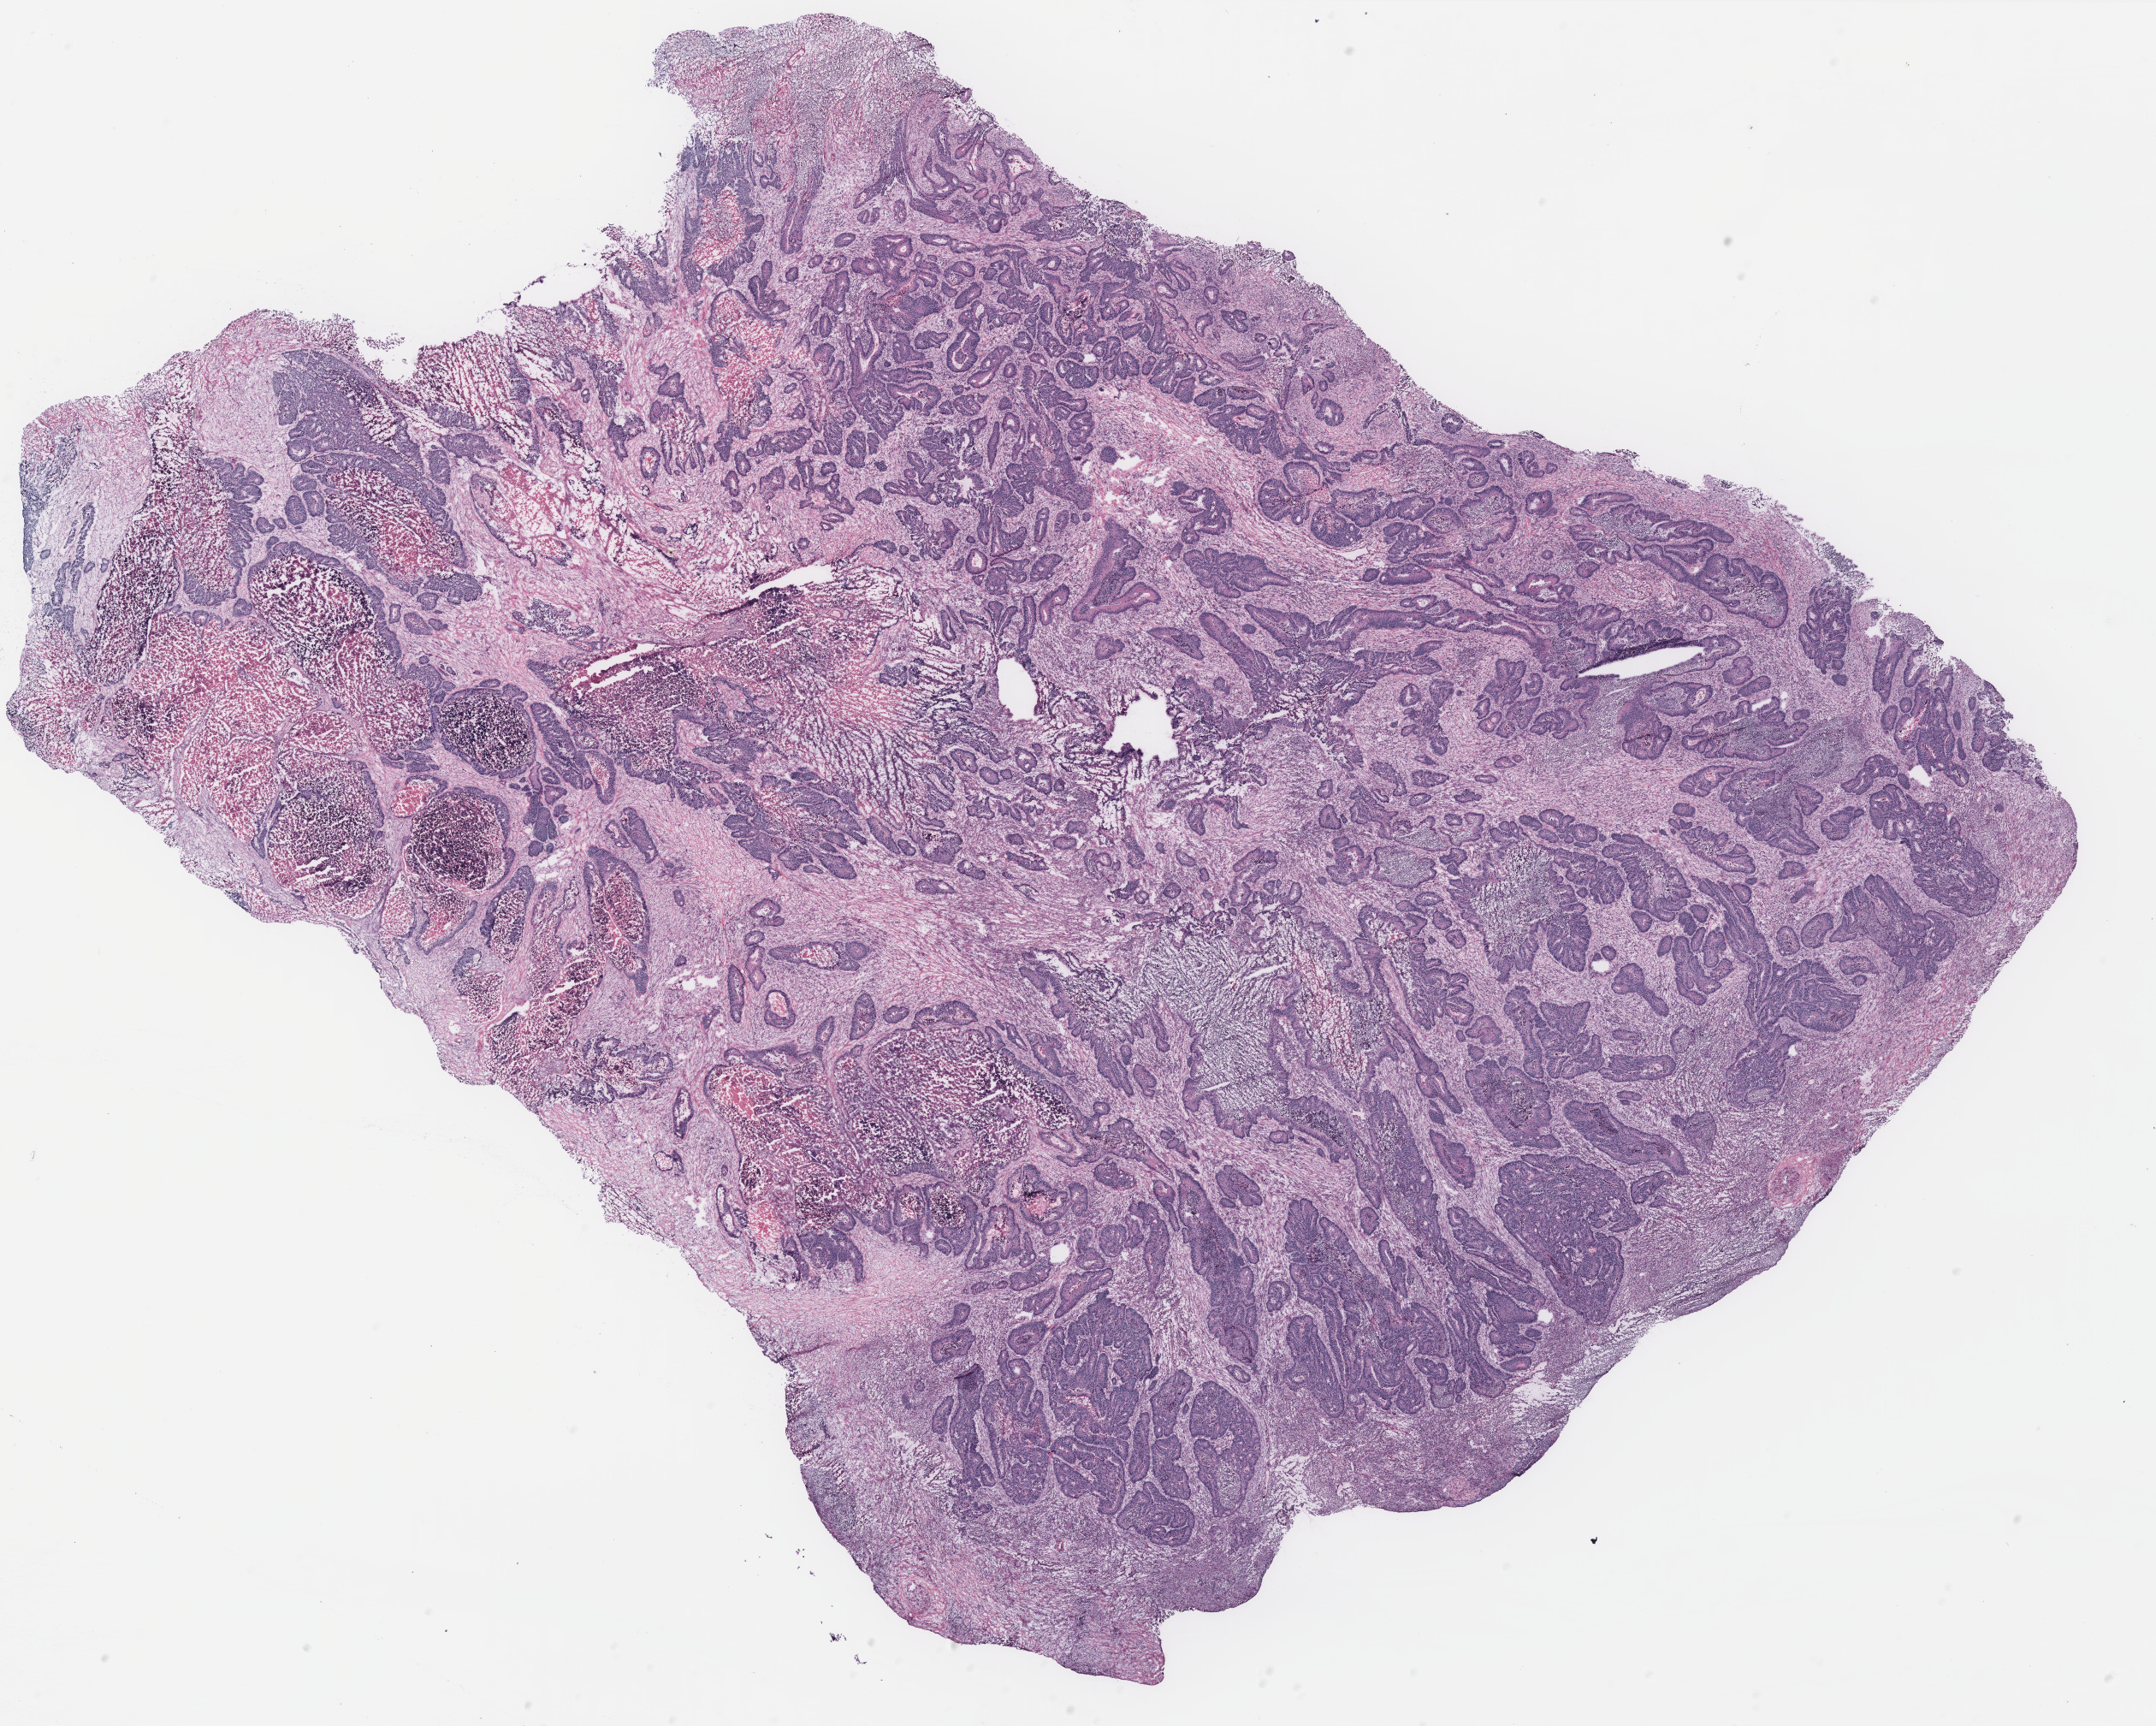
Whole-slide histology image, H&E, low-resolution overview of the scanned area, about 20.2 x 16.1 mm (acquisition: 40x scan), colon, tissue type not recorded.
Patient diagnosis (cohort enrolment): colon cancer (colon).